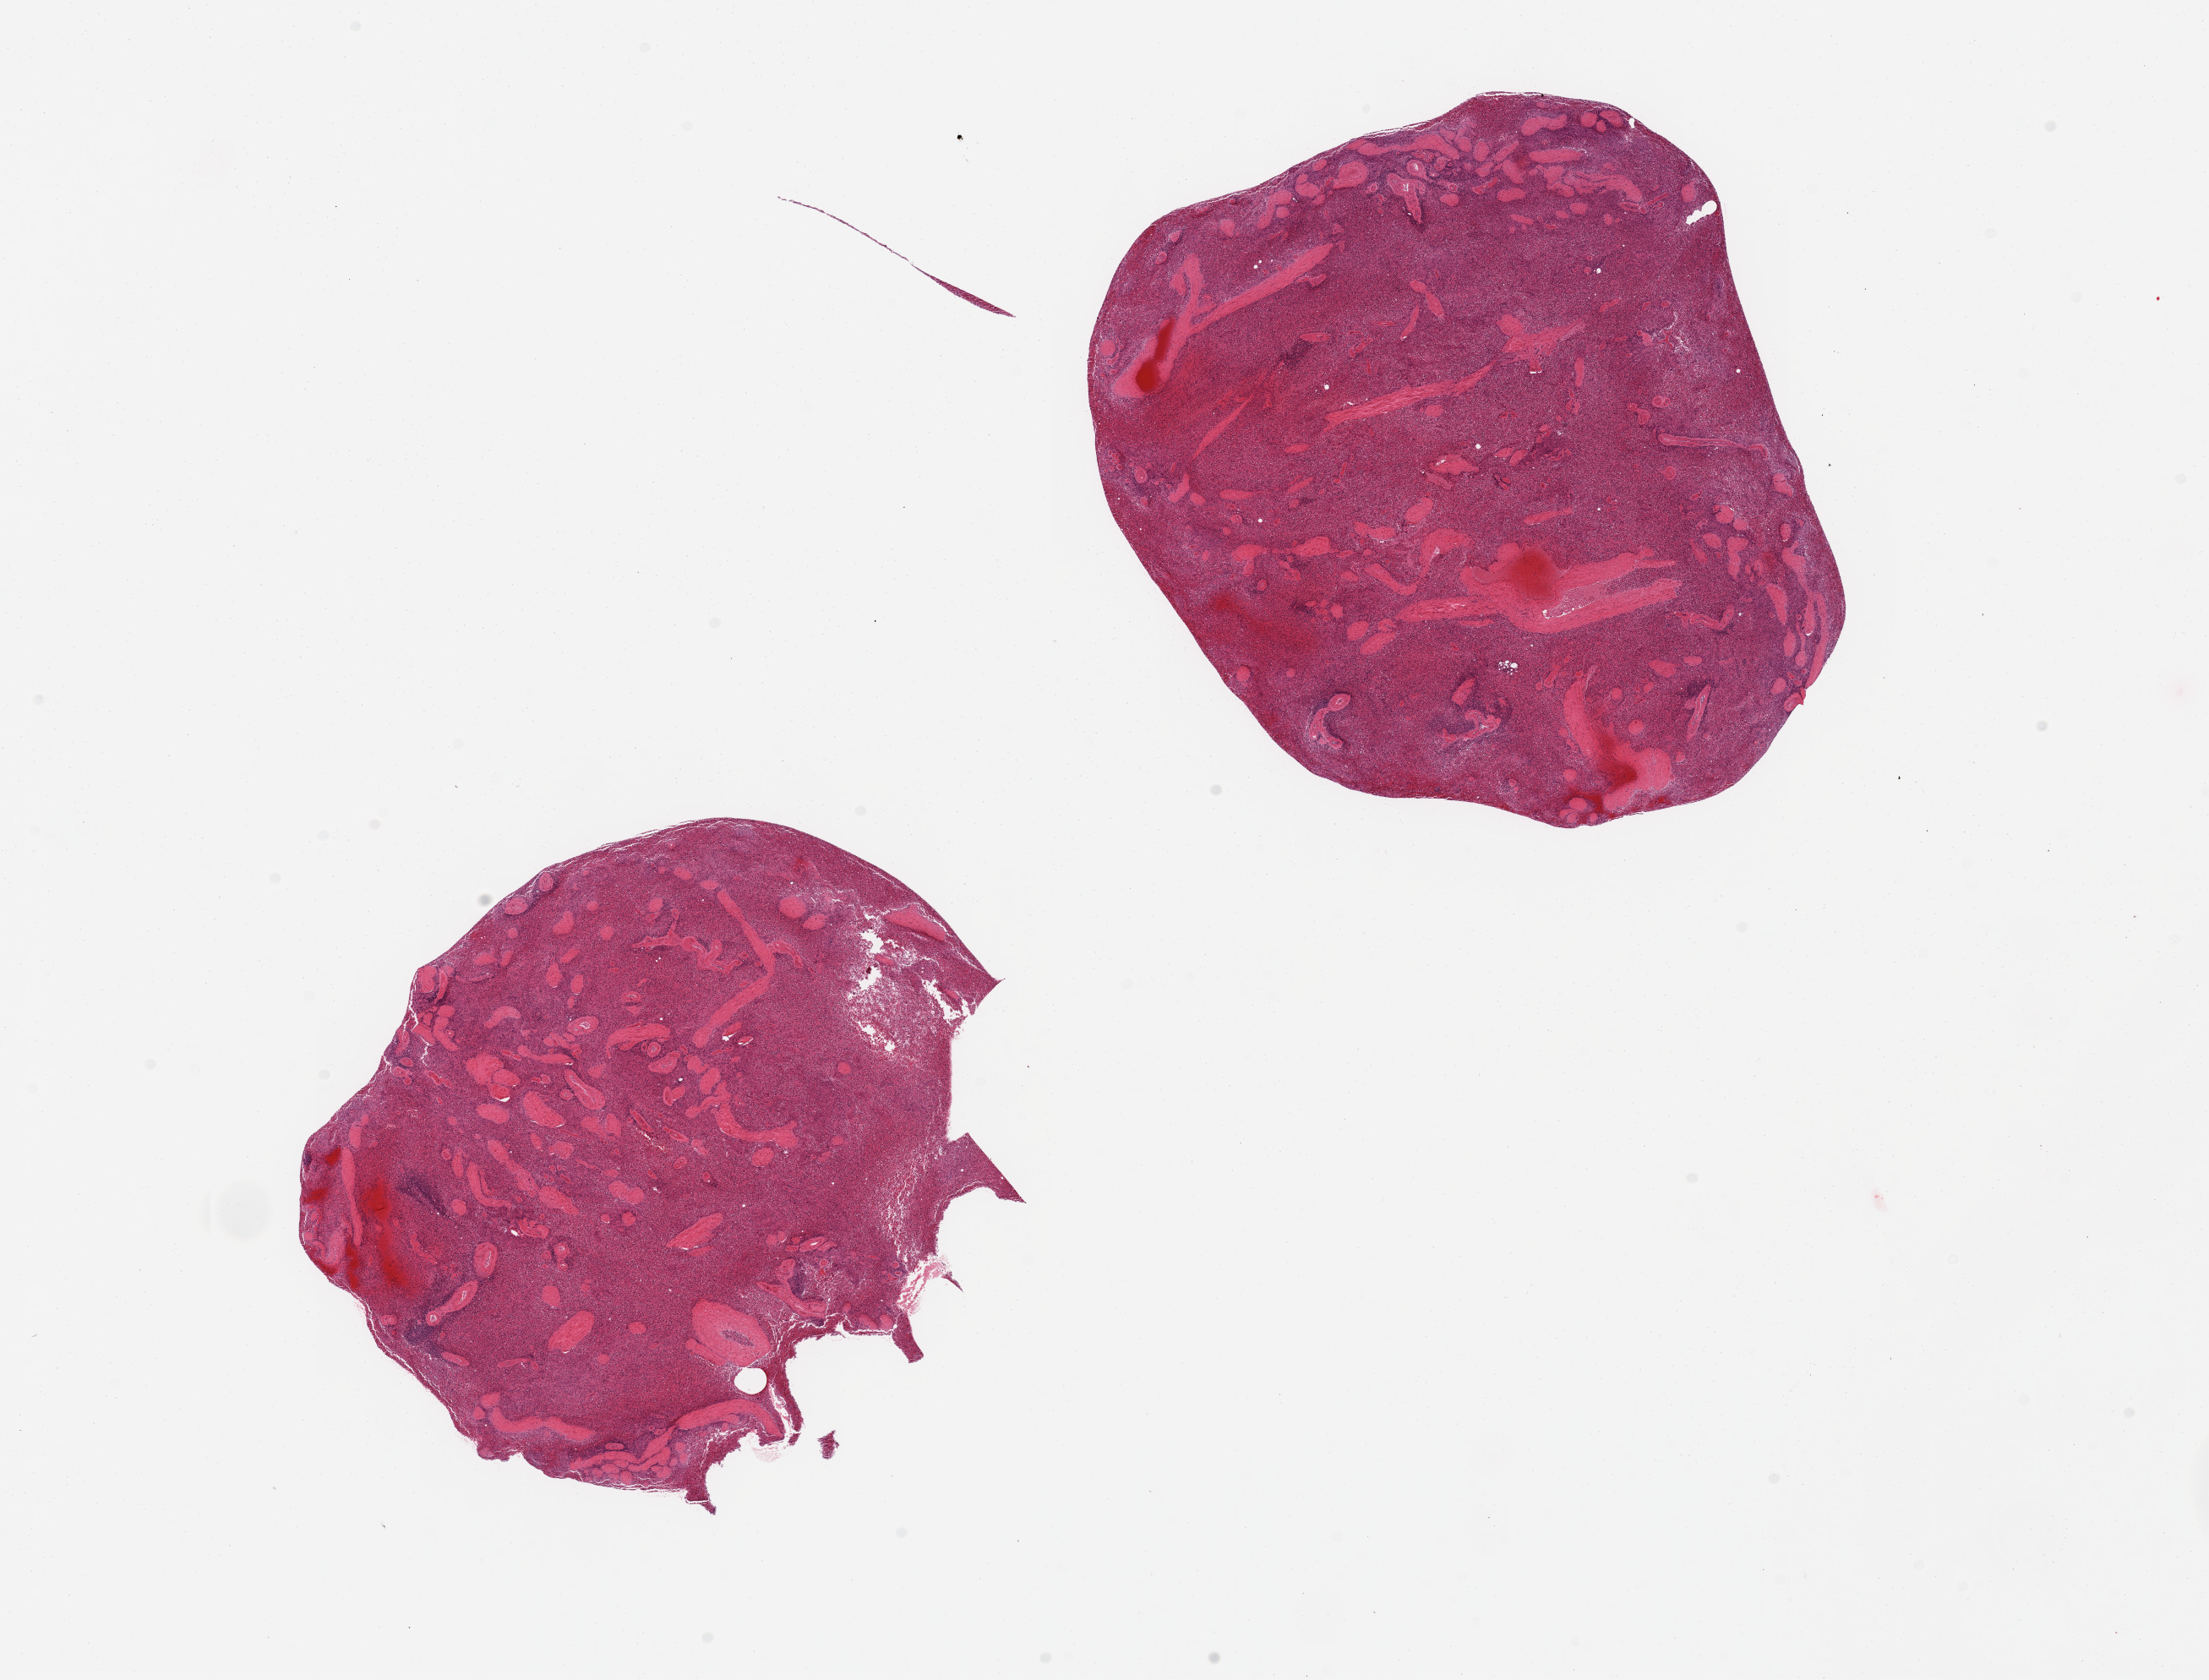
Digitized H&E-stained section — whole scanned area (about 20.7 x 15.7 mm) shown as a low-resolution overview; PAXgene-fixed, paraffin-embedded tissue; target tissue: spleen; donor tissue sample. Donor: male.
Reviewer comment on this tissue sample: 2 pieces, marked congestion, badly autolyzed.